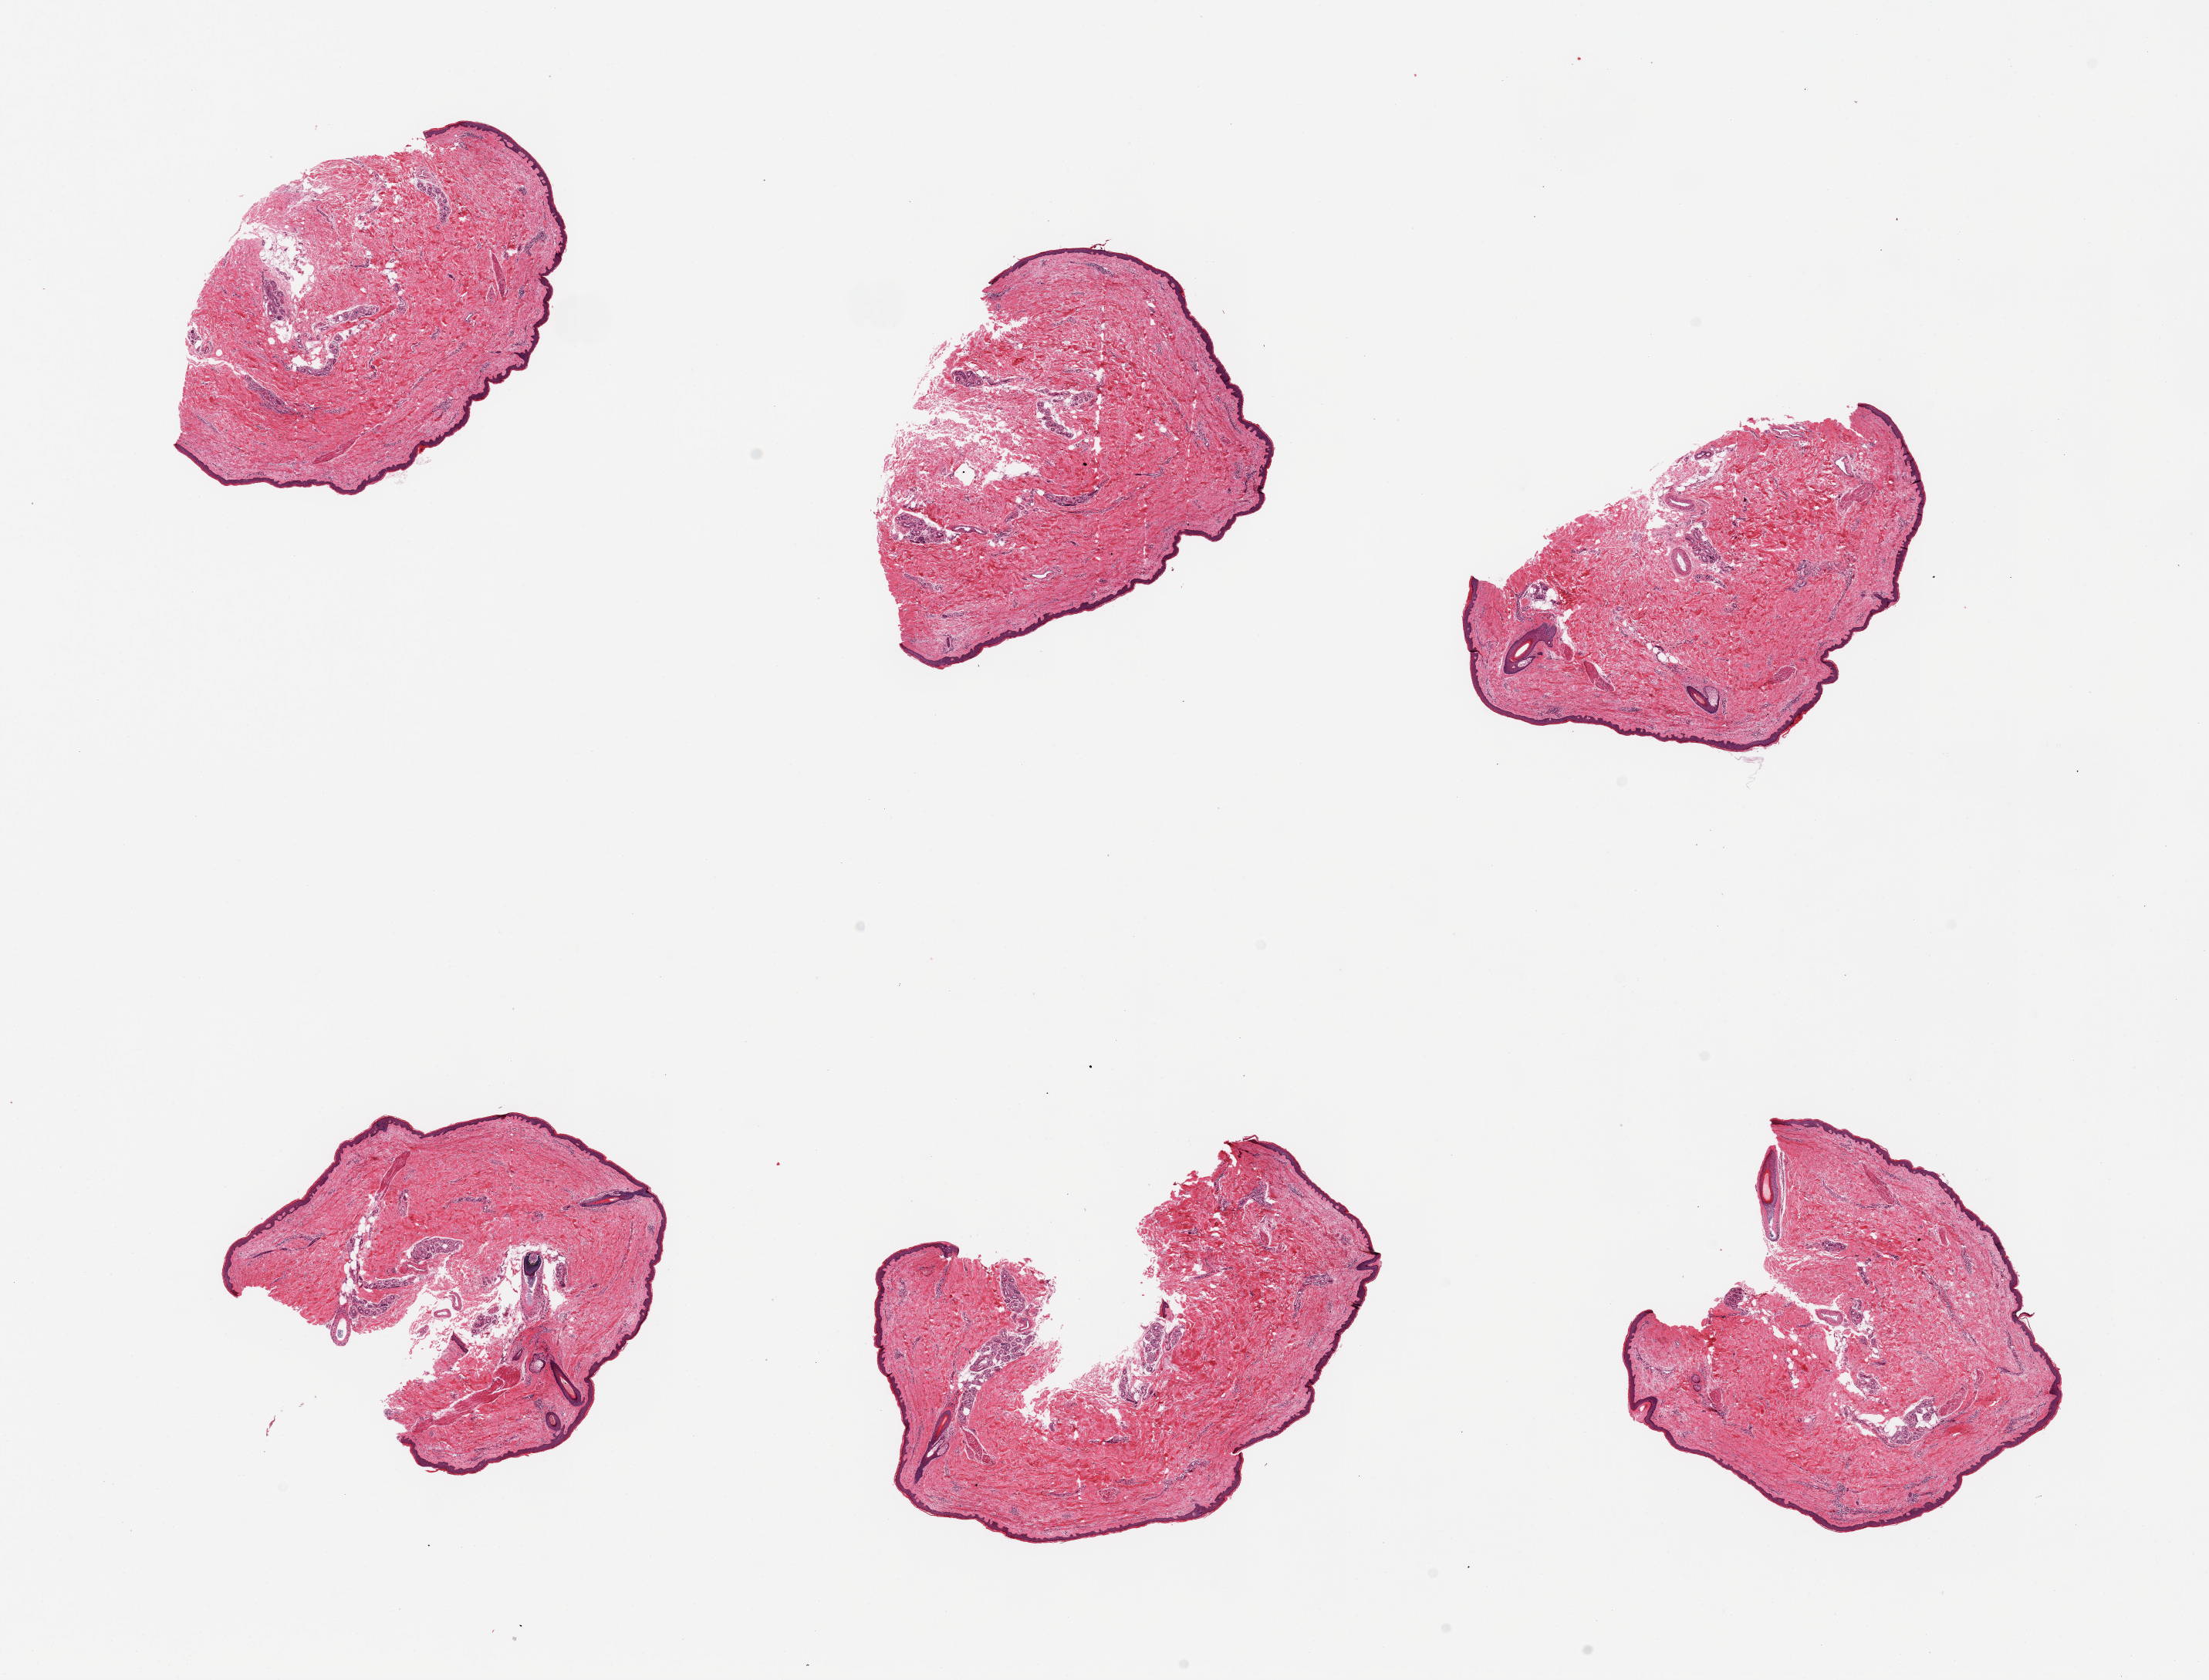
Whole-slide image, haematoxylin and eosin stain, shown as a low-resolution overview of the whole scanned area (about 22.6 x 17.2 mm, slide scanned at 20x). PAXgene-fixed, paraffin-embedded tissue. Section of skin of lower leg (target tissue). Tissue donor sample. Donor: male.
Pathologist's review note for this sample: 6 pieces well trimmed; 60.63um thickness of the epidermis.